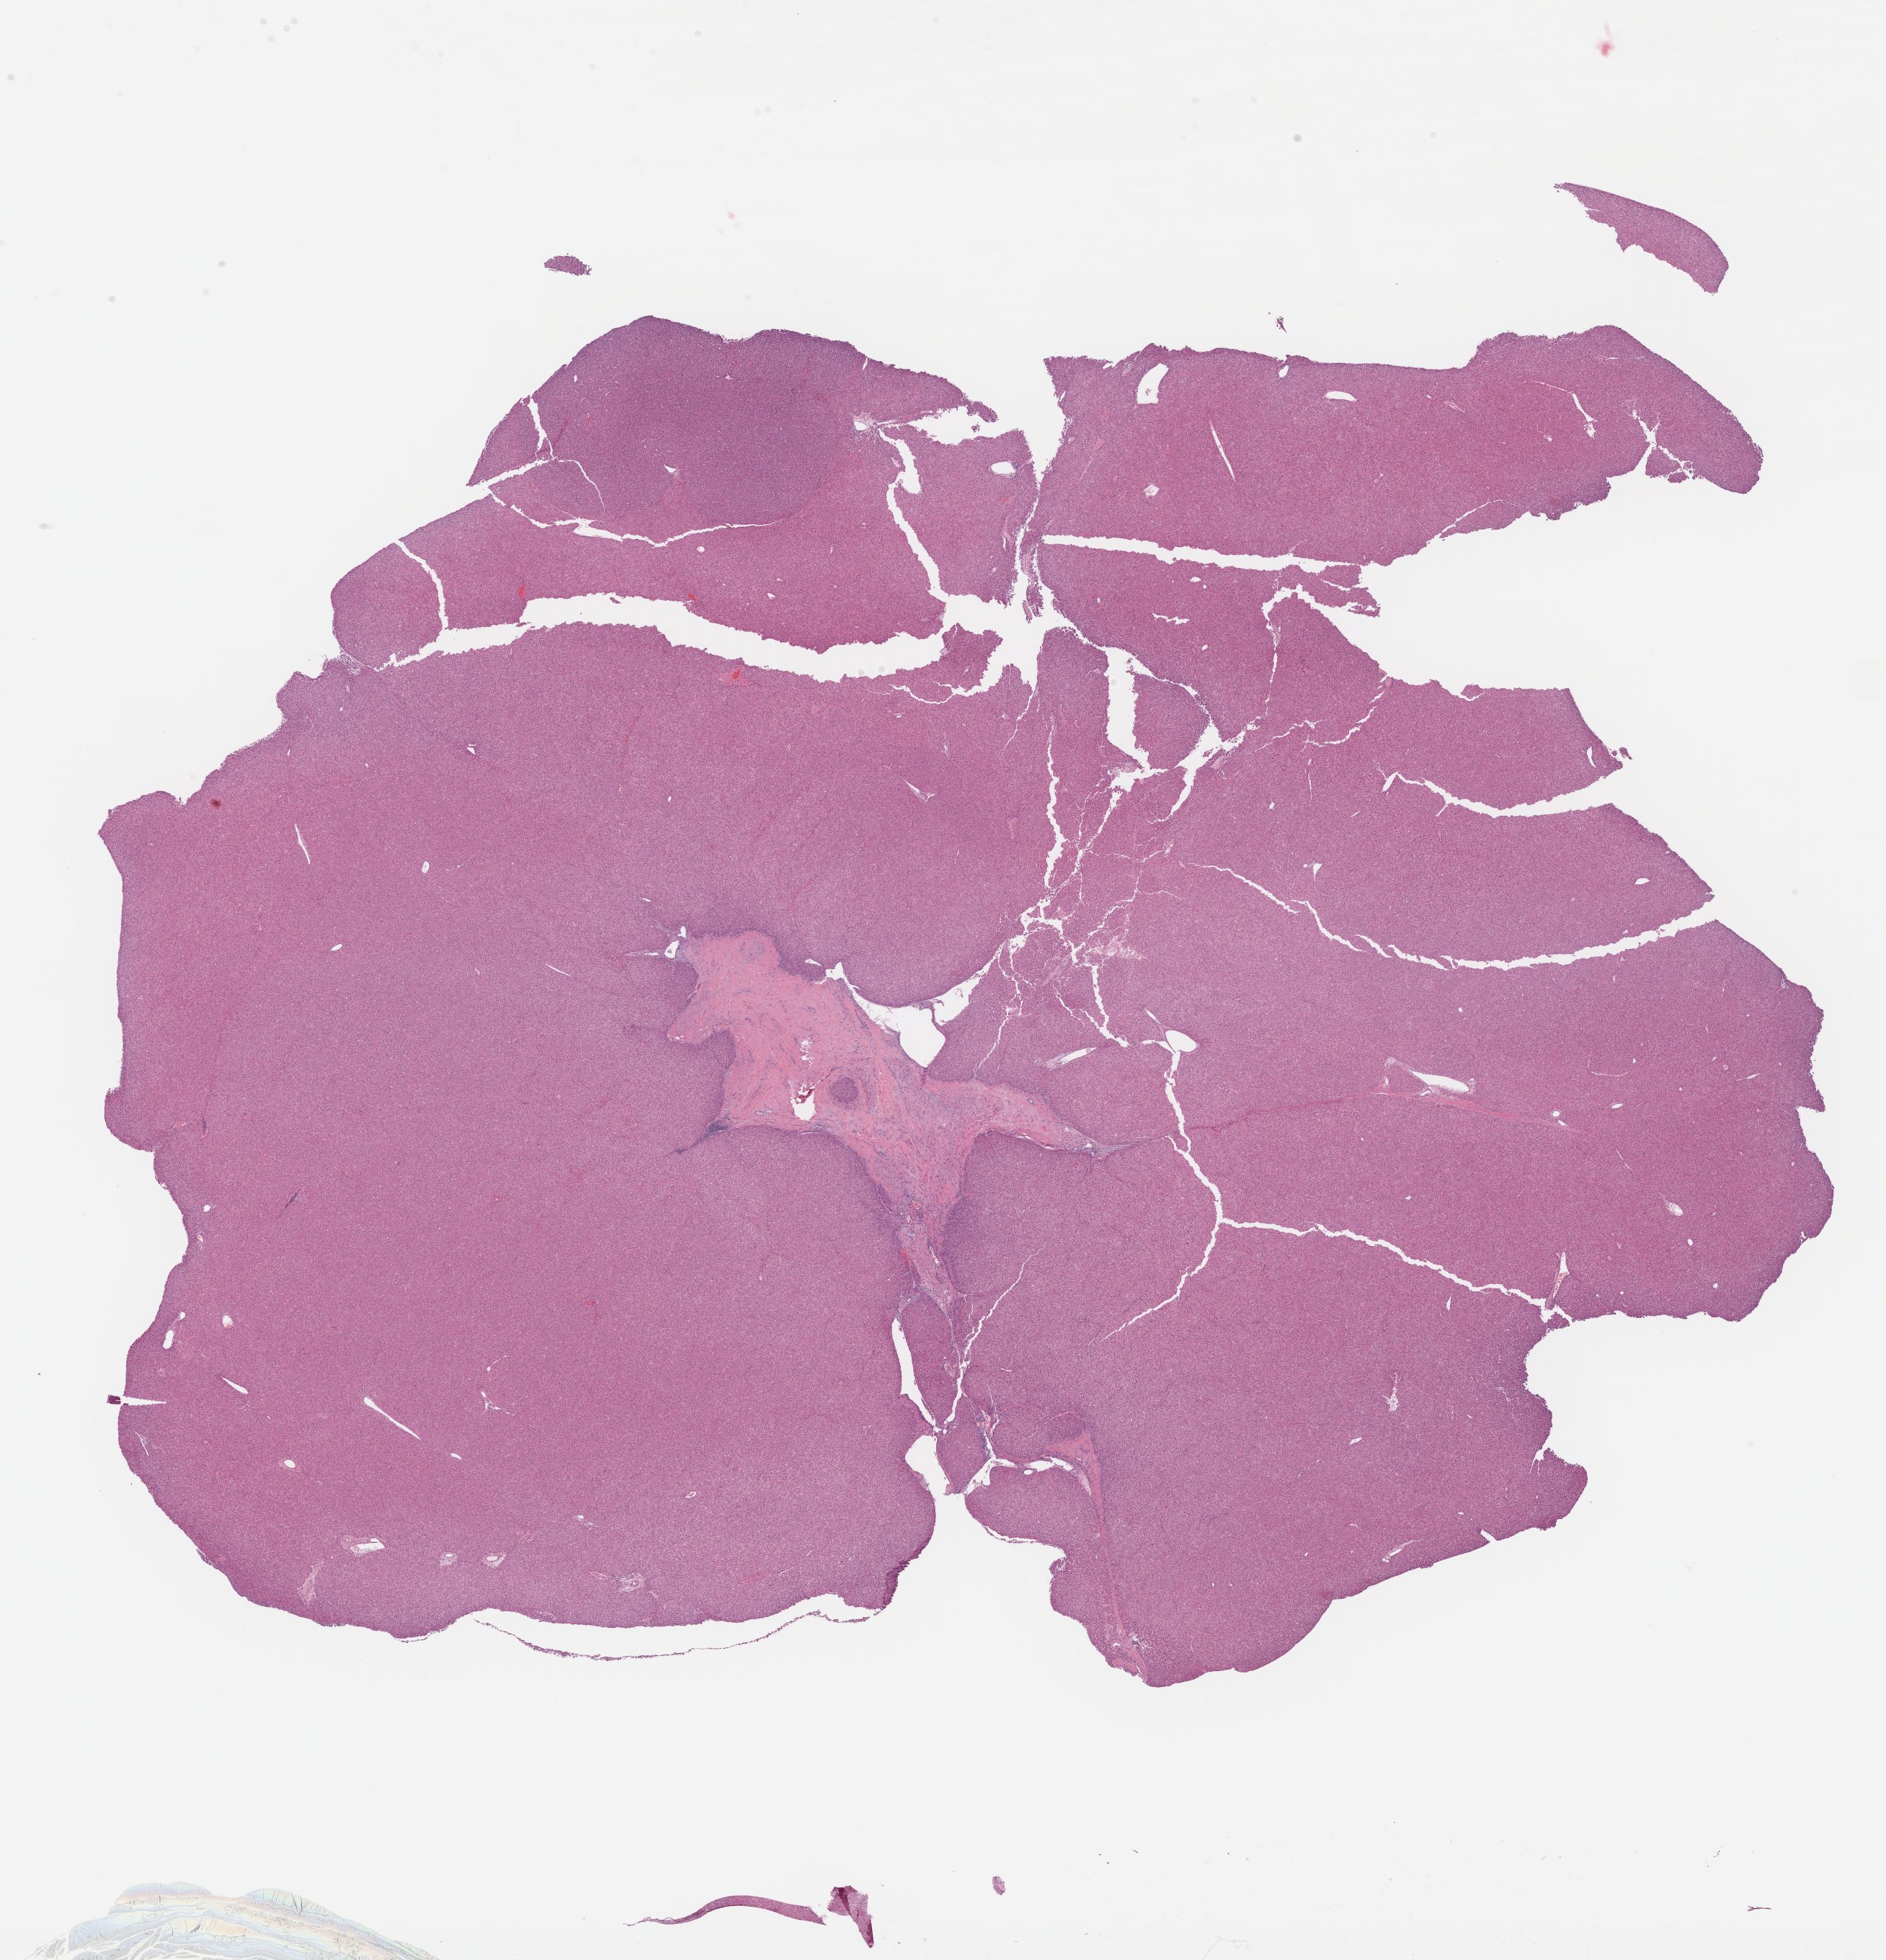
Whole-slide histology image, H&E-stained, low-resolution overview of the scanned area, about 21.2 x 22.0 mm; formalin-fixed paraffin-embedded (FFPE) diagnostic section; sample: primary tumour, liver. Patient: female, age at initial diagnosis 68 years. Histologic grade: G1 (well differentiated).
• AJCC pathologic stage: II
• pathologic diagnosis: Hepatocellular carcinoma, NOS